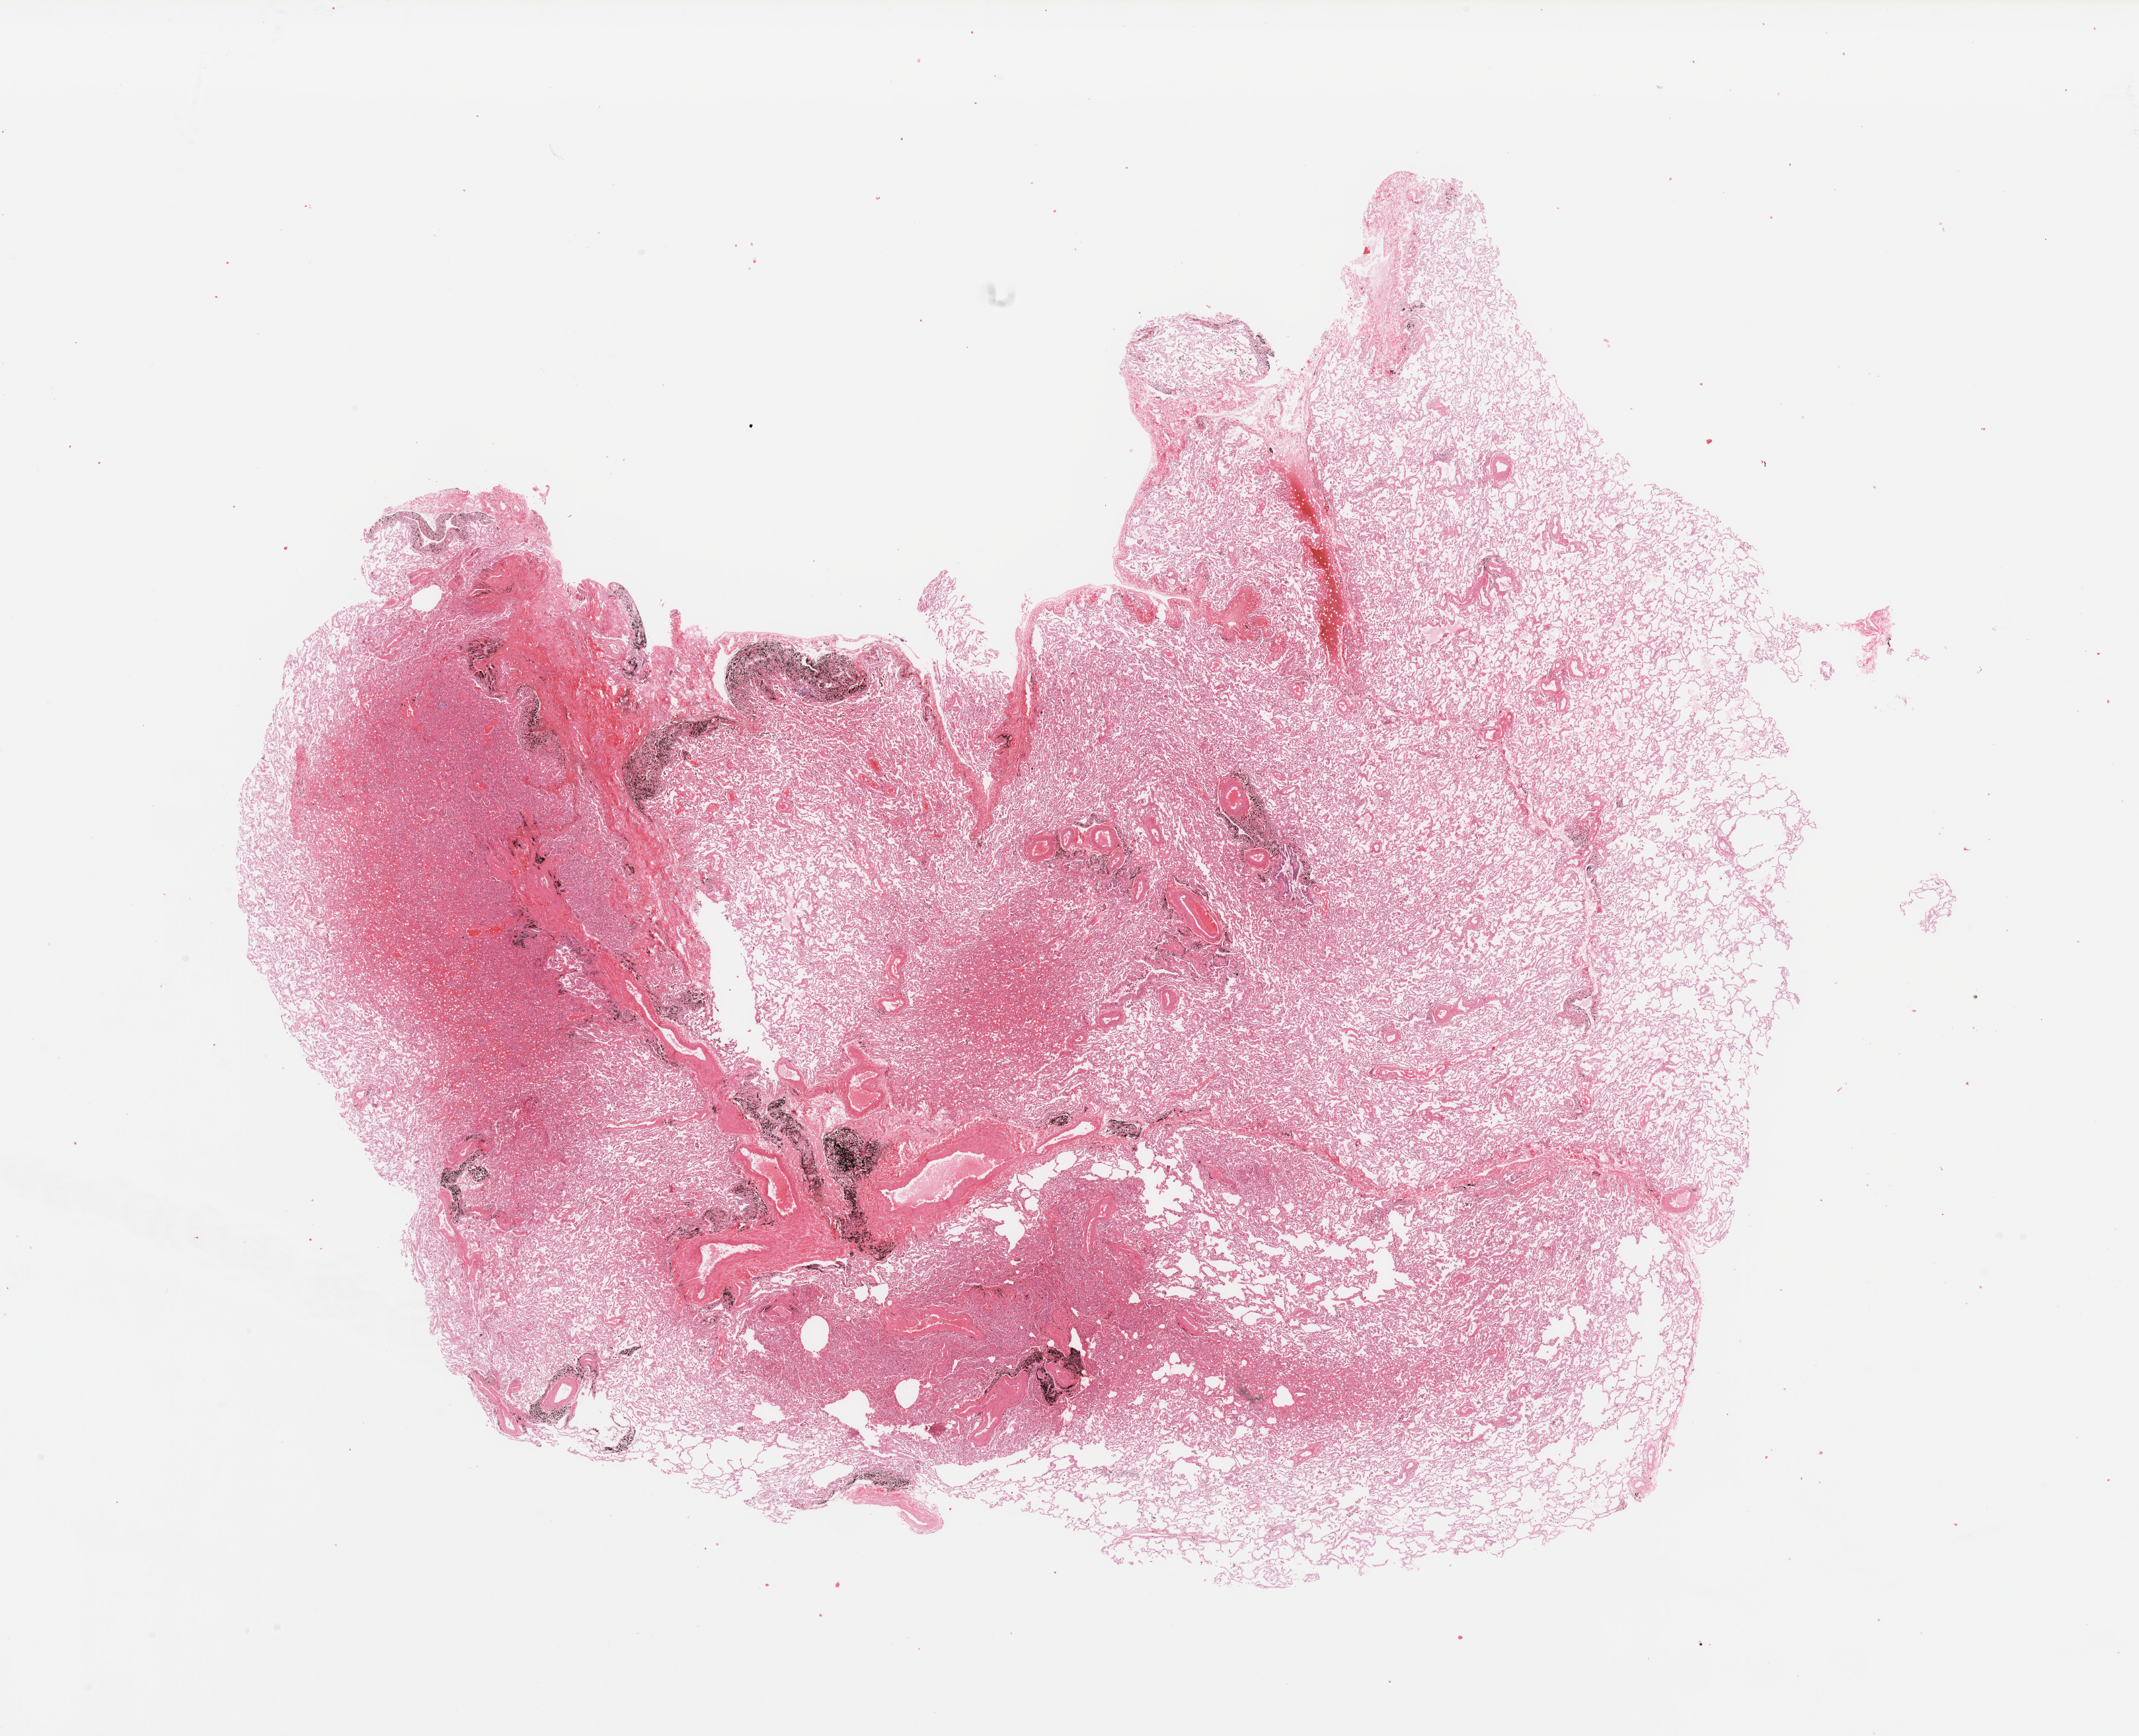
Digitized H&E-stained tissue section (whole slide), low-resolution overview of the scanned area, about 25.6 x 20.8 mm (acquisition: 20x scan). Normal (non-tumour) tissue sample, lung. Male, 62 y/o.
This section: normal (non-tumour) tissue from the same patient. Patient diagnosis: Adenocarcinoma, NOS.